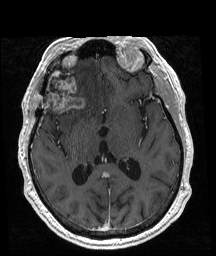
Brain MRI from a brain-tumour surgery series, one axial slice. Position 99 of 192 along the scan axis. T1-weighted post-contrast. 1 mm slice thickness. 216 × 256 image matrix. From the clinical record (not read from this slice): histopathology: Glioblastoma; WHO grade: 4; IDH mutation: no; tumour location: Right Frontal.
Structures marked on this image (expert manual segmentation):
- previous resection cavity: bounding box (x1, y1, x2, y2) in pixels: (50, 76, 64, 93)